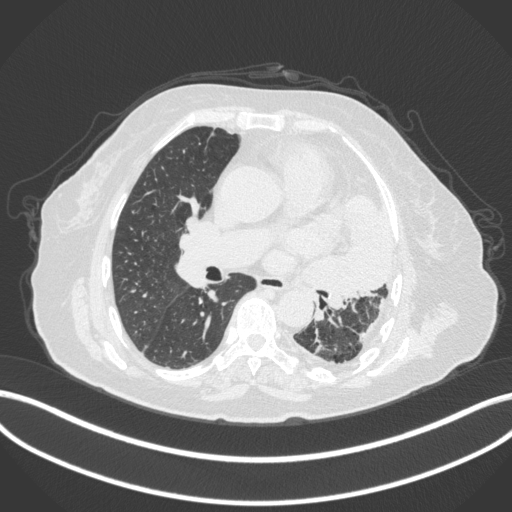
Chest CT, one axial slice; position 197 of 399 along the scan axis; 120 kVp; lung window (W 1500 / L -600 HU); 1 mm slice thickness; 512 × 512 image matrix. Female patient, age 75 years. From the clinical record (not read from this slice): clinical TNM (as recorded): T3 N3 M1.
Structures marked on this image (bounding box drawn by a radiologist):
- lung tumour (recorded histology: adenocarcinoma): box from (x=309, y=188) to (x=392, y=300) px